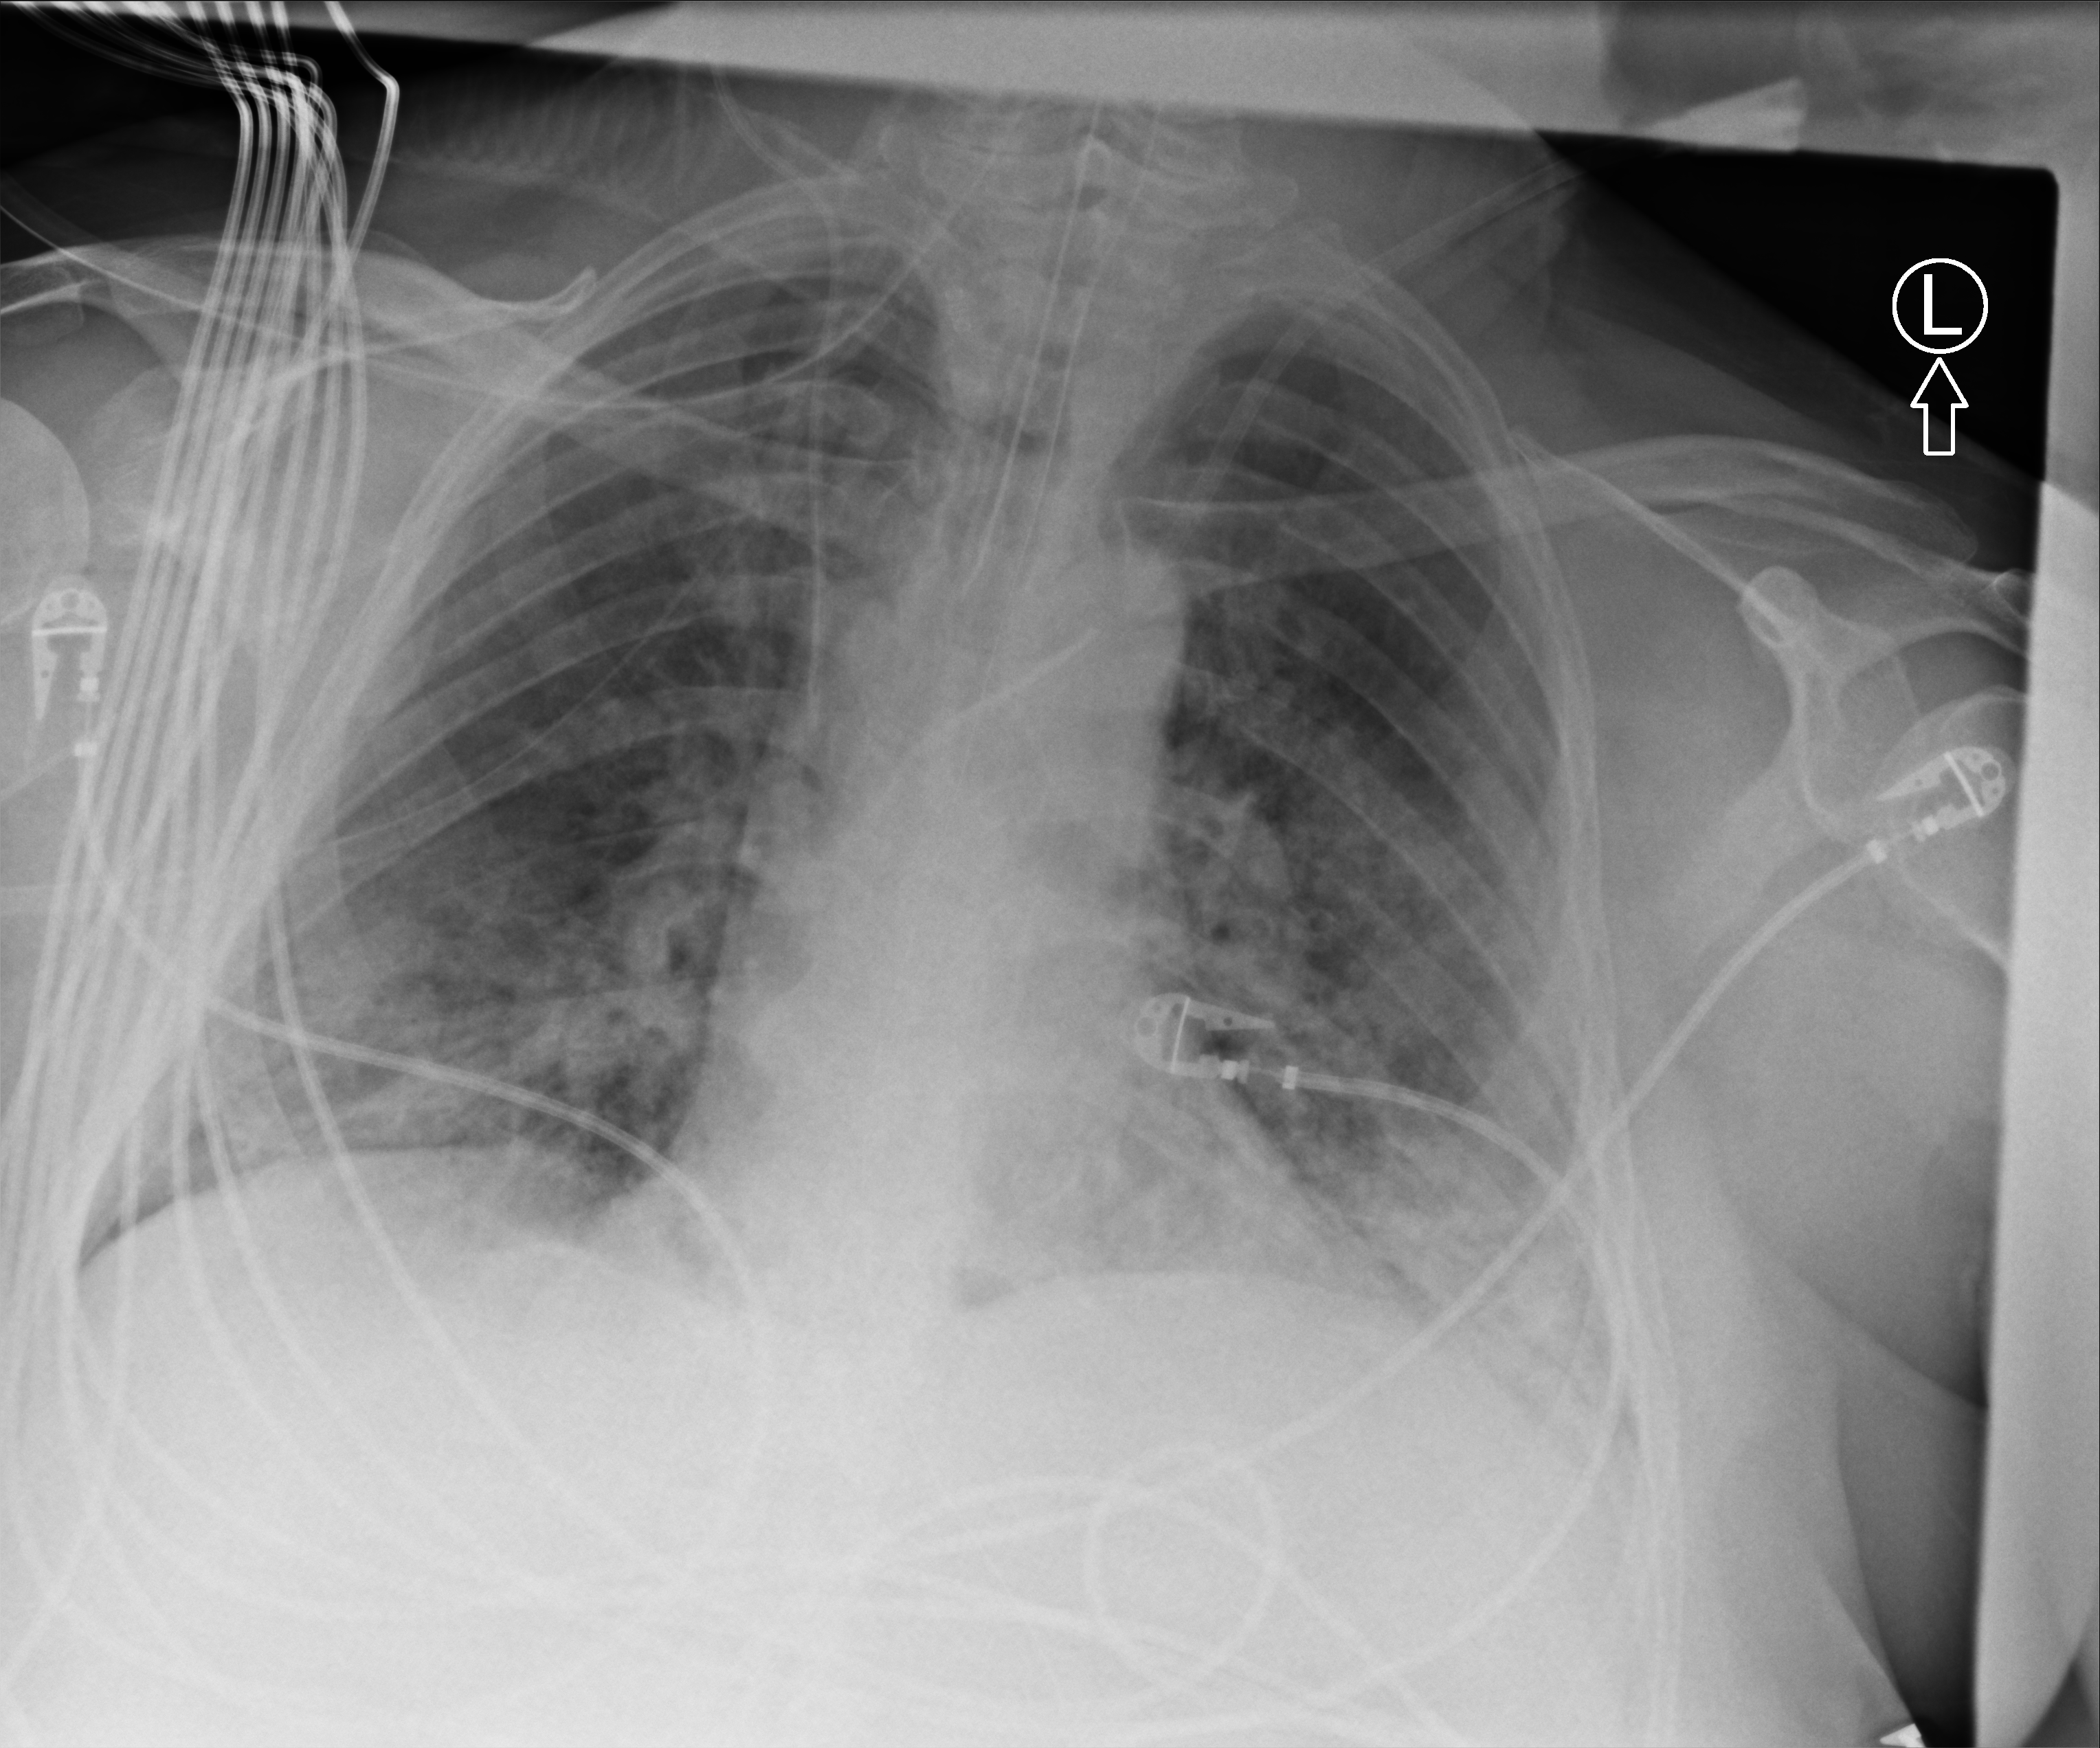
Bedside chest radiograph (computed radiography). Male patient hospitalised with COVID-19, age 18–59 years.
From the hospital-stay record, not from the radiograph (when in the stay this image was taken is not recorded): mechanically ventilated during this hospital stay: yes.